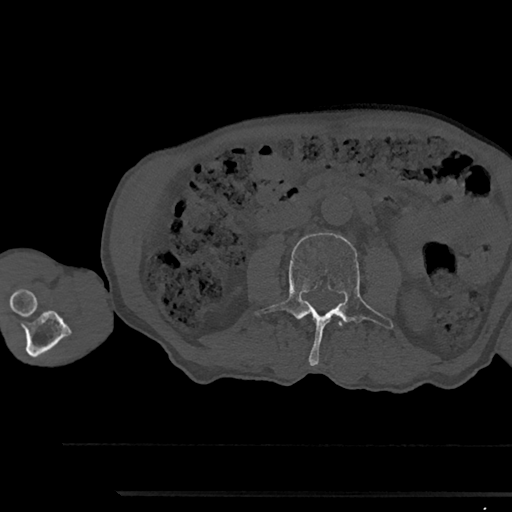
CT including the spine, one axial slice; slice 496 of 797 in the series (ordered by position); reconstruction kernel Br40s/3; 120 kVp; bone window (W 1800 / L 400 HU); 0.5 mm slice thickness; 512 × 512 image matrix, field of view 367 × 367 mm. Male patient, age 79 years. From the clinical record (not read from this slice): primary cancer: prostate.
Annotated regions visible in this slice (semi-automatic segmentation, software-assisted and operator-edited):
- L2 vertebra: bounding box (x1, y1, x2, y2) in pixels: (338, 322, 342, 326)
- L3 vertebra: (254, 233, 393, 366)